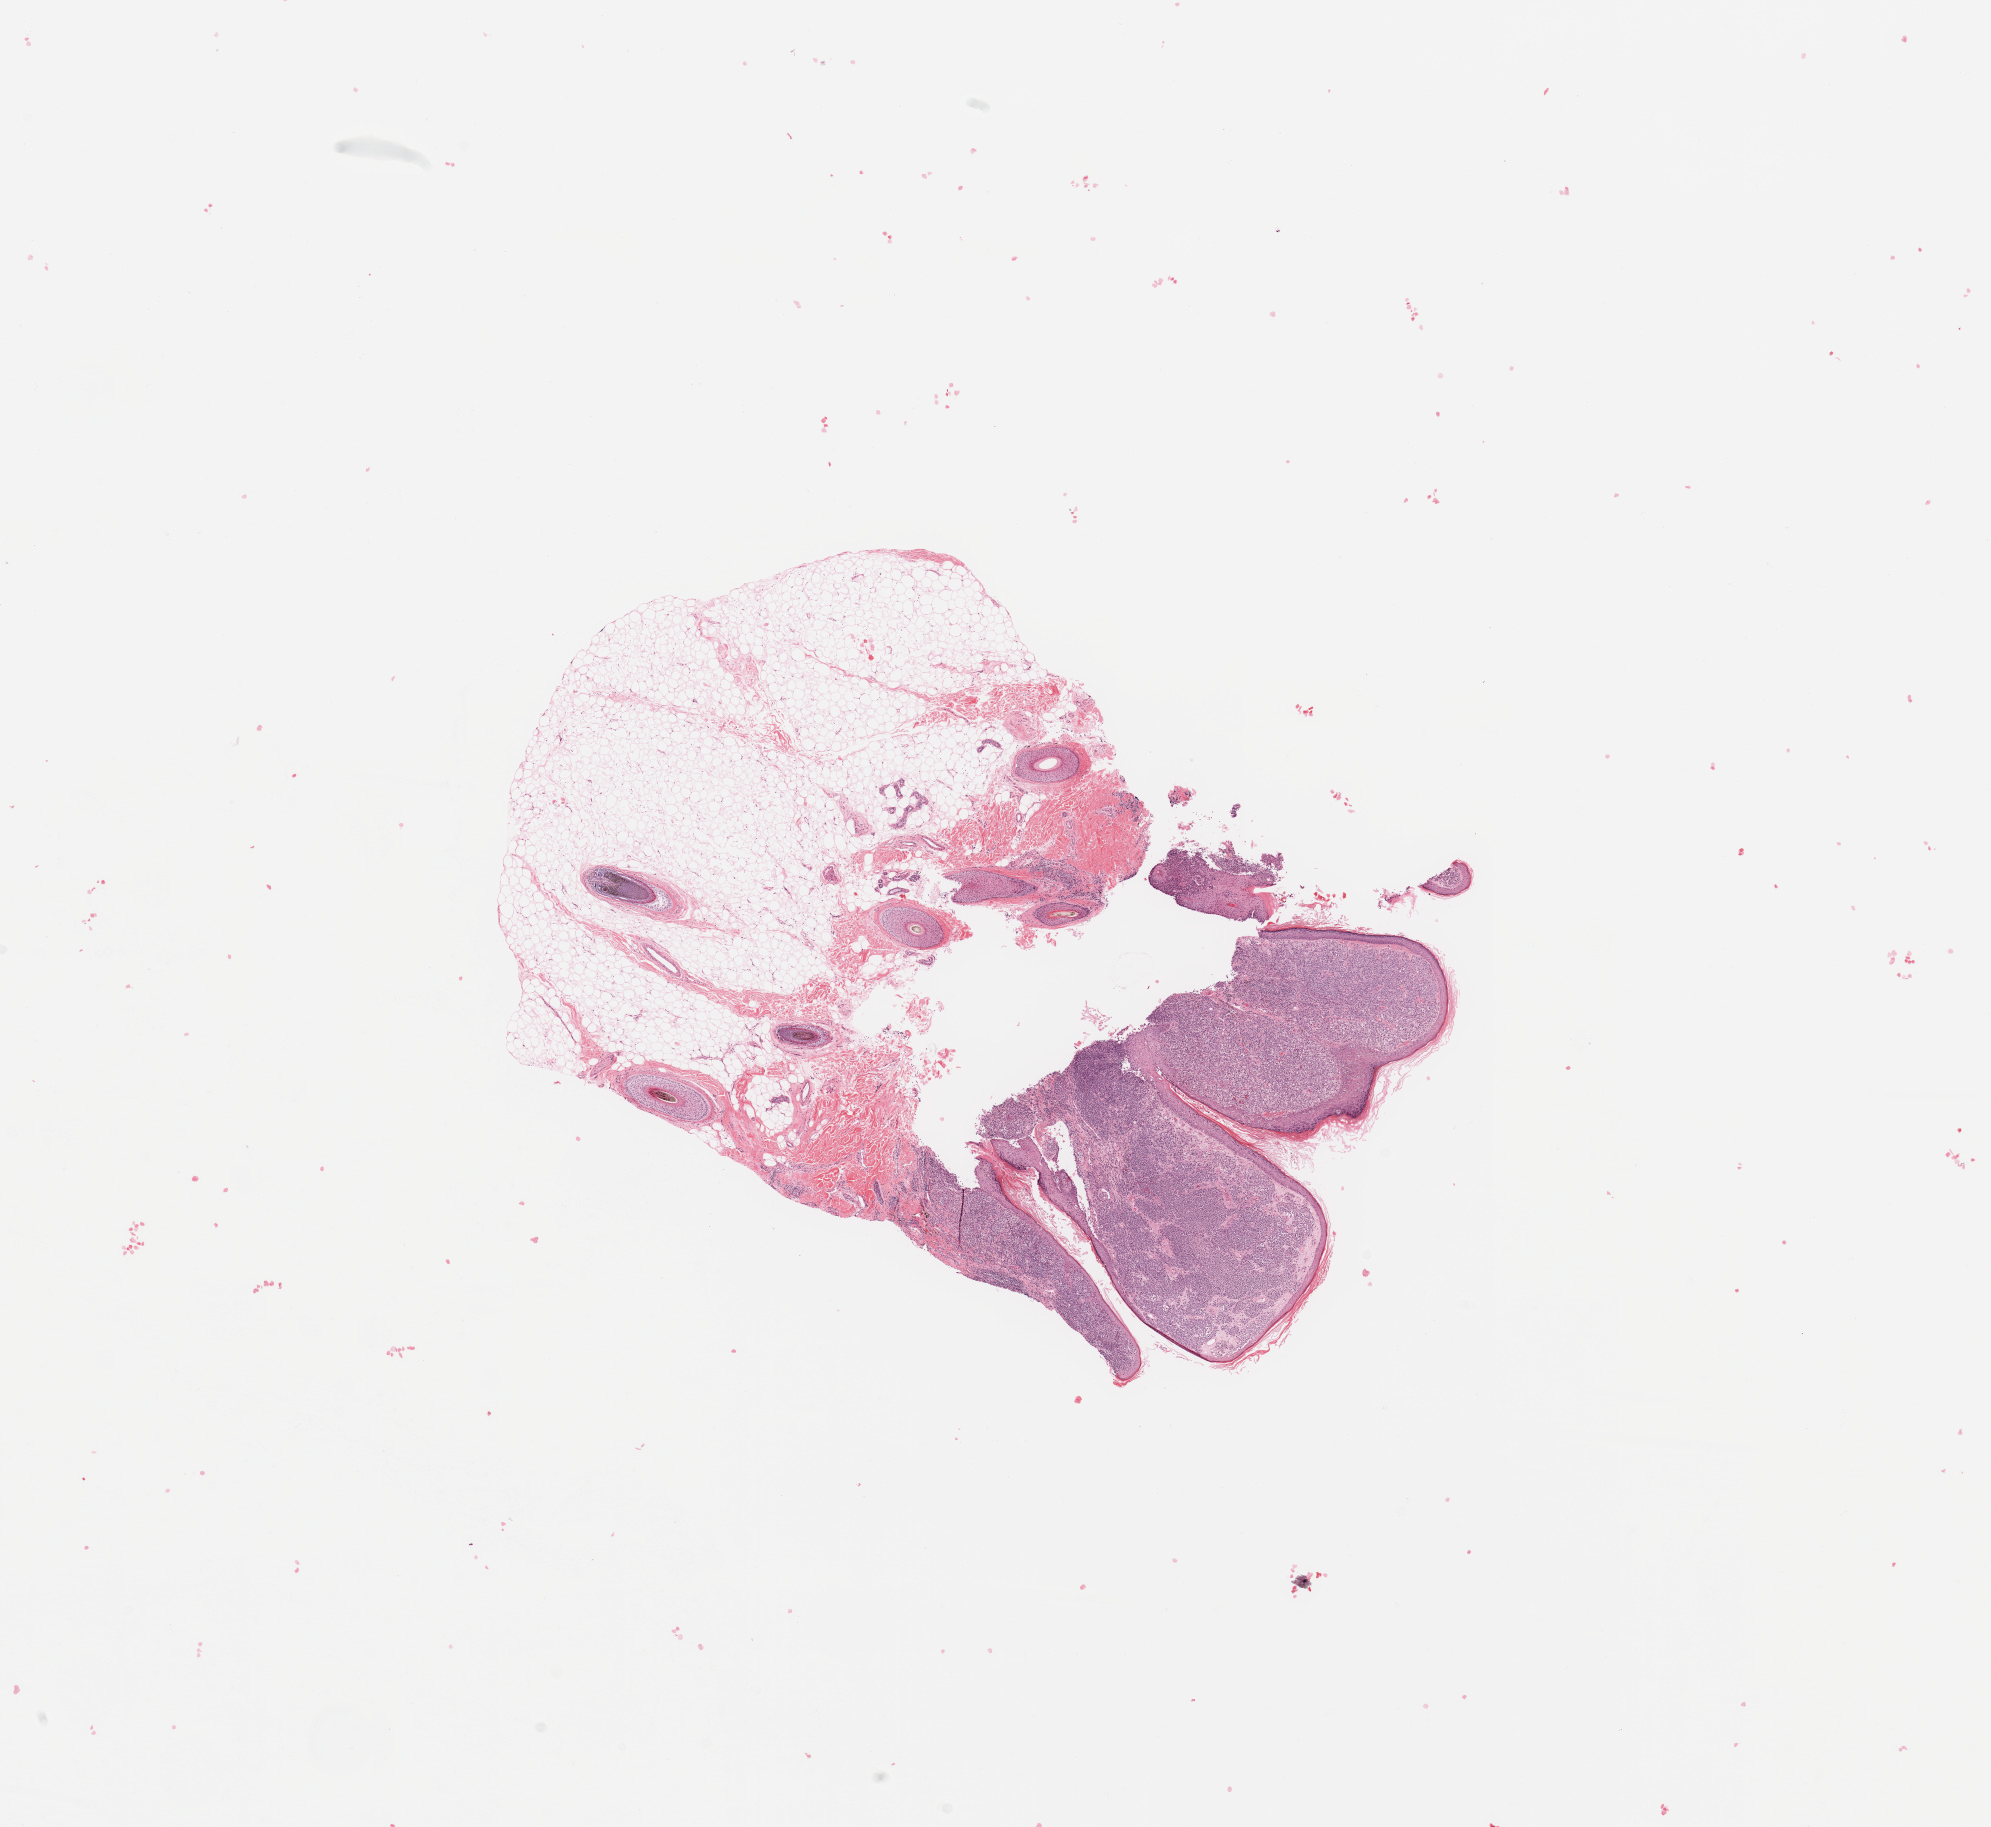
Whole-slide histology image, H&E — shown as a low-resolution overview of the whole scanned area (about 15.8 x 14.5 mm); tumour tissue sample, sampled site: head & neck. Patient: female, age 73 years. Pathologist review of this section (percent, as recorded): tumour nuclei 85%, necrosis 0%.
AJCC pathologic stage: IIA. Diagnosis: Malignant melanoma, NOS. Primary tumour site (as recorded): head & neck.